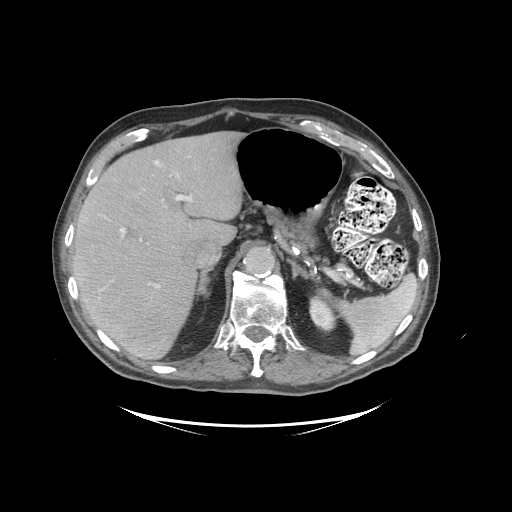
Contrast-enhanced abdominal CT (liver protocol), one axial slice. Slice 68 of 99 in the series (ordered by position). Reconstruction kernel STANDARD. 140 kVp. Soft-tissue window (W 400 / L 40 HU). 2.5 mm slice thickness. 512 × 512 image matrix, field of view 460 × 460 mm. Case-level facts recorded for this patient, not image findings: diagnosis: hepatocellular carcinoma (patient treated with transarterial chemoembolisation; whether this scan precedes or follows treatment is not stated here); TNM stage (as recorded): Stage-I; Child-Pugh class: A; tumour differentiation: moderately differentiated.
Outlined on this slice (semi-automatic segmentation, software-assisted and operator-edited):
- liver parenchyma outside the tumour (the mass and vessels are separate outlines, so this box may not span the whole liver): bounding box (x1, y1, x2, y2) in pixels: (72, 132, 242, 358)
- liver vessels: (78, 161, 192, 288)